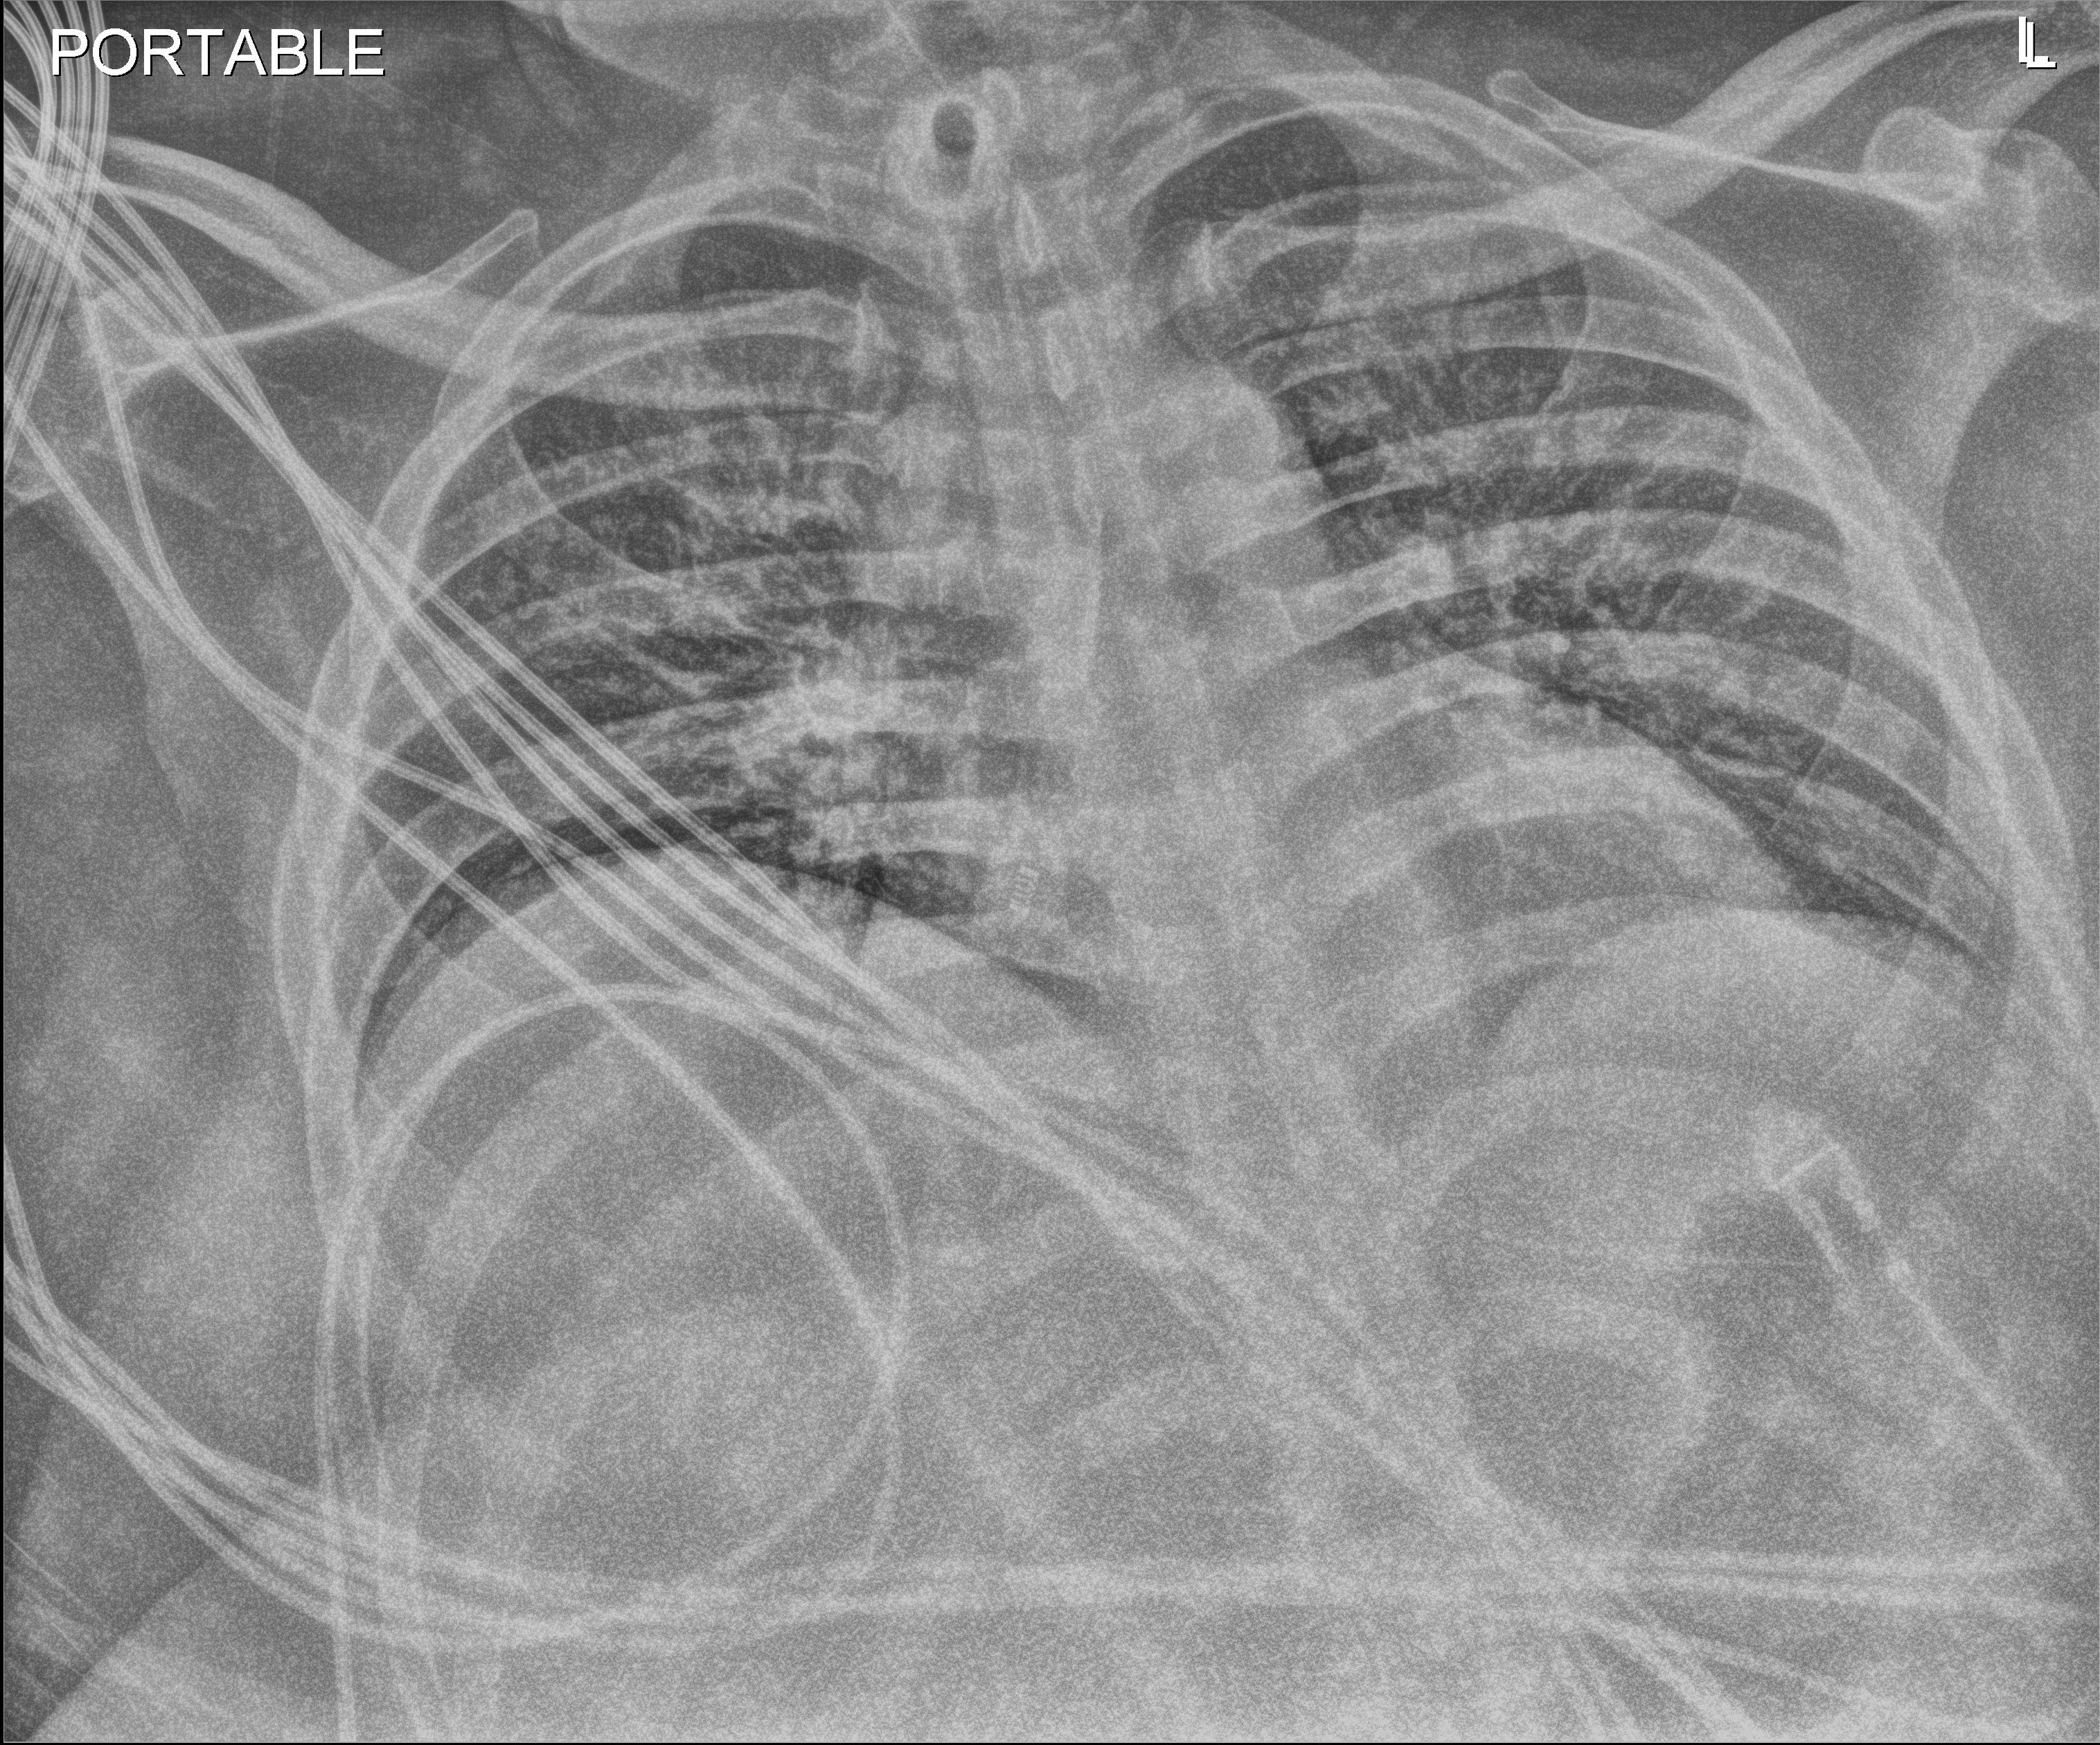
Chest X-ray (portable); anteroposterior (AP) projection. Male patient hospitalised with COVID-19, age 18–59 years.
Hospital-stay facts (about this admission, not read from this image; timing relative to this image not recorded): smoking status (admission record): never; mechanically ventilated during this hospital stay: yes.